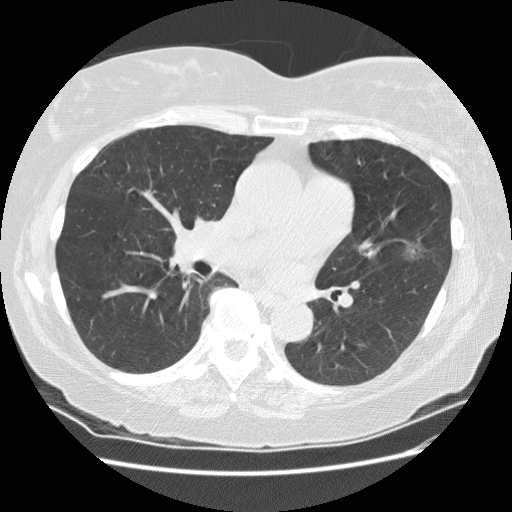
Chest CT (low-dose screening protocol), one axial image, second screening round (one year after baseline), lung window (W 1500 / L -600 HU), 2.5 mm slice thickness, standard (soft-tissue) reconstruction kernel (STANDARD). Female participant, aged 71 years at enrolment. Former smoker at enrolment.
Expert reader's lesion annotation, bounding box (x1, y1, x2, y2) in pixels: (389, 225, 439, 265). The exam's reader record, not a measurement of the box and not confirmed to be the same lesion: non-calcified nodule or mass ≥4 mm, lingula, 13 × 13 mm, poorly defined margins, ground glass attenuation, pre-existing on the prior screen: yes; interval growth: yes. Official screen result: positive, change unspecified: nodule(s) >= 4 mm or enlarging nodule(s), mass(es), or other non-specific abnormalities suspicious for lung cancer. Later outcome: lung cancer diagnosed 26 days after this screen — adenocarcinoma, NOS, left upper lobe, well differentiated (G1), stage IA (AJCC 6th edition), 11 mm at pathology.